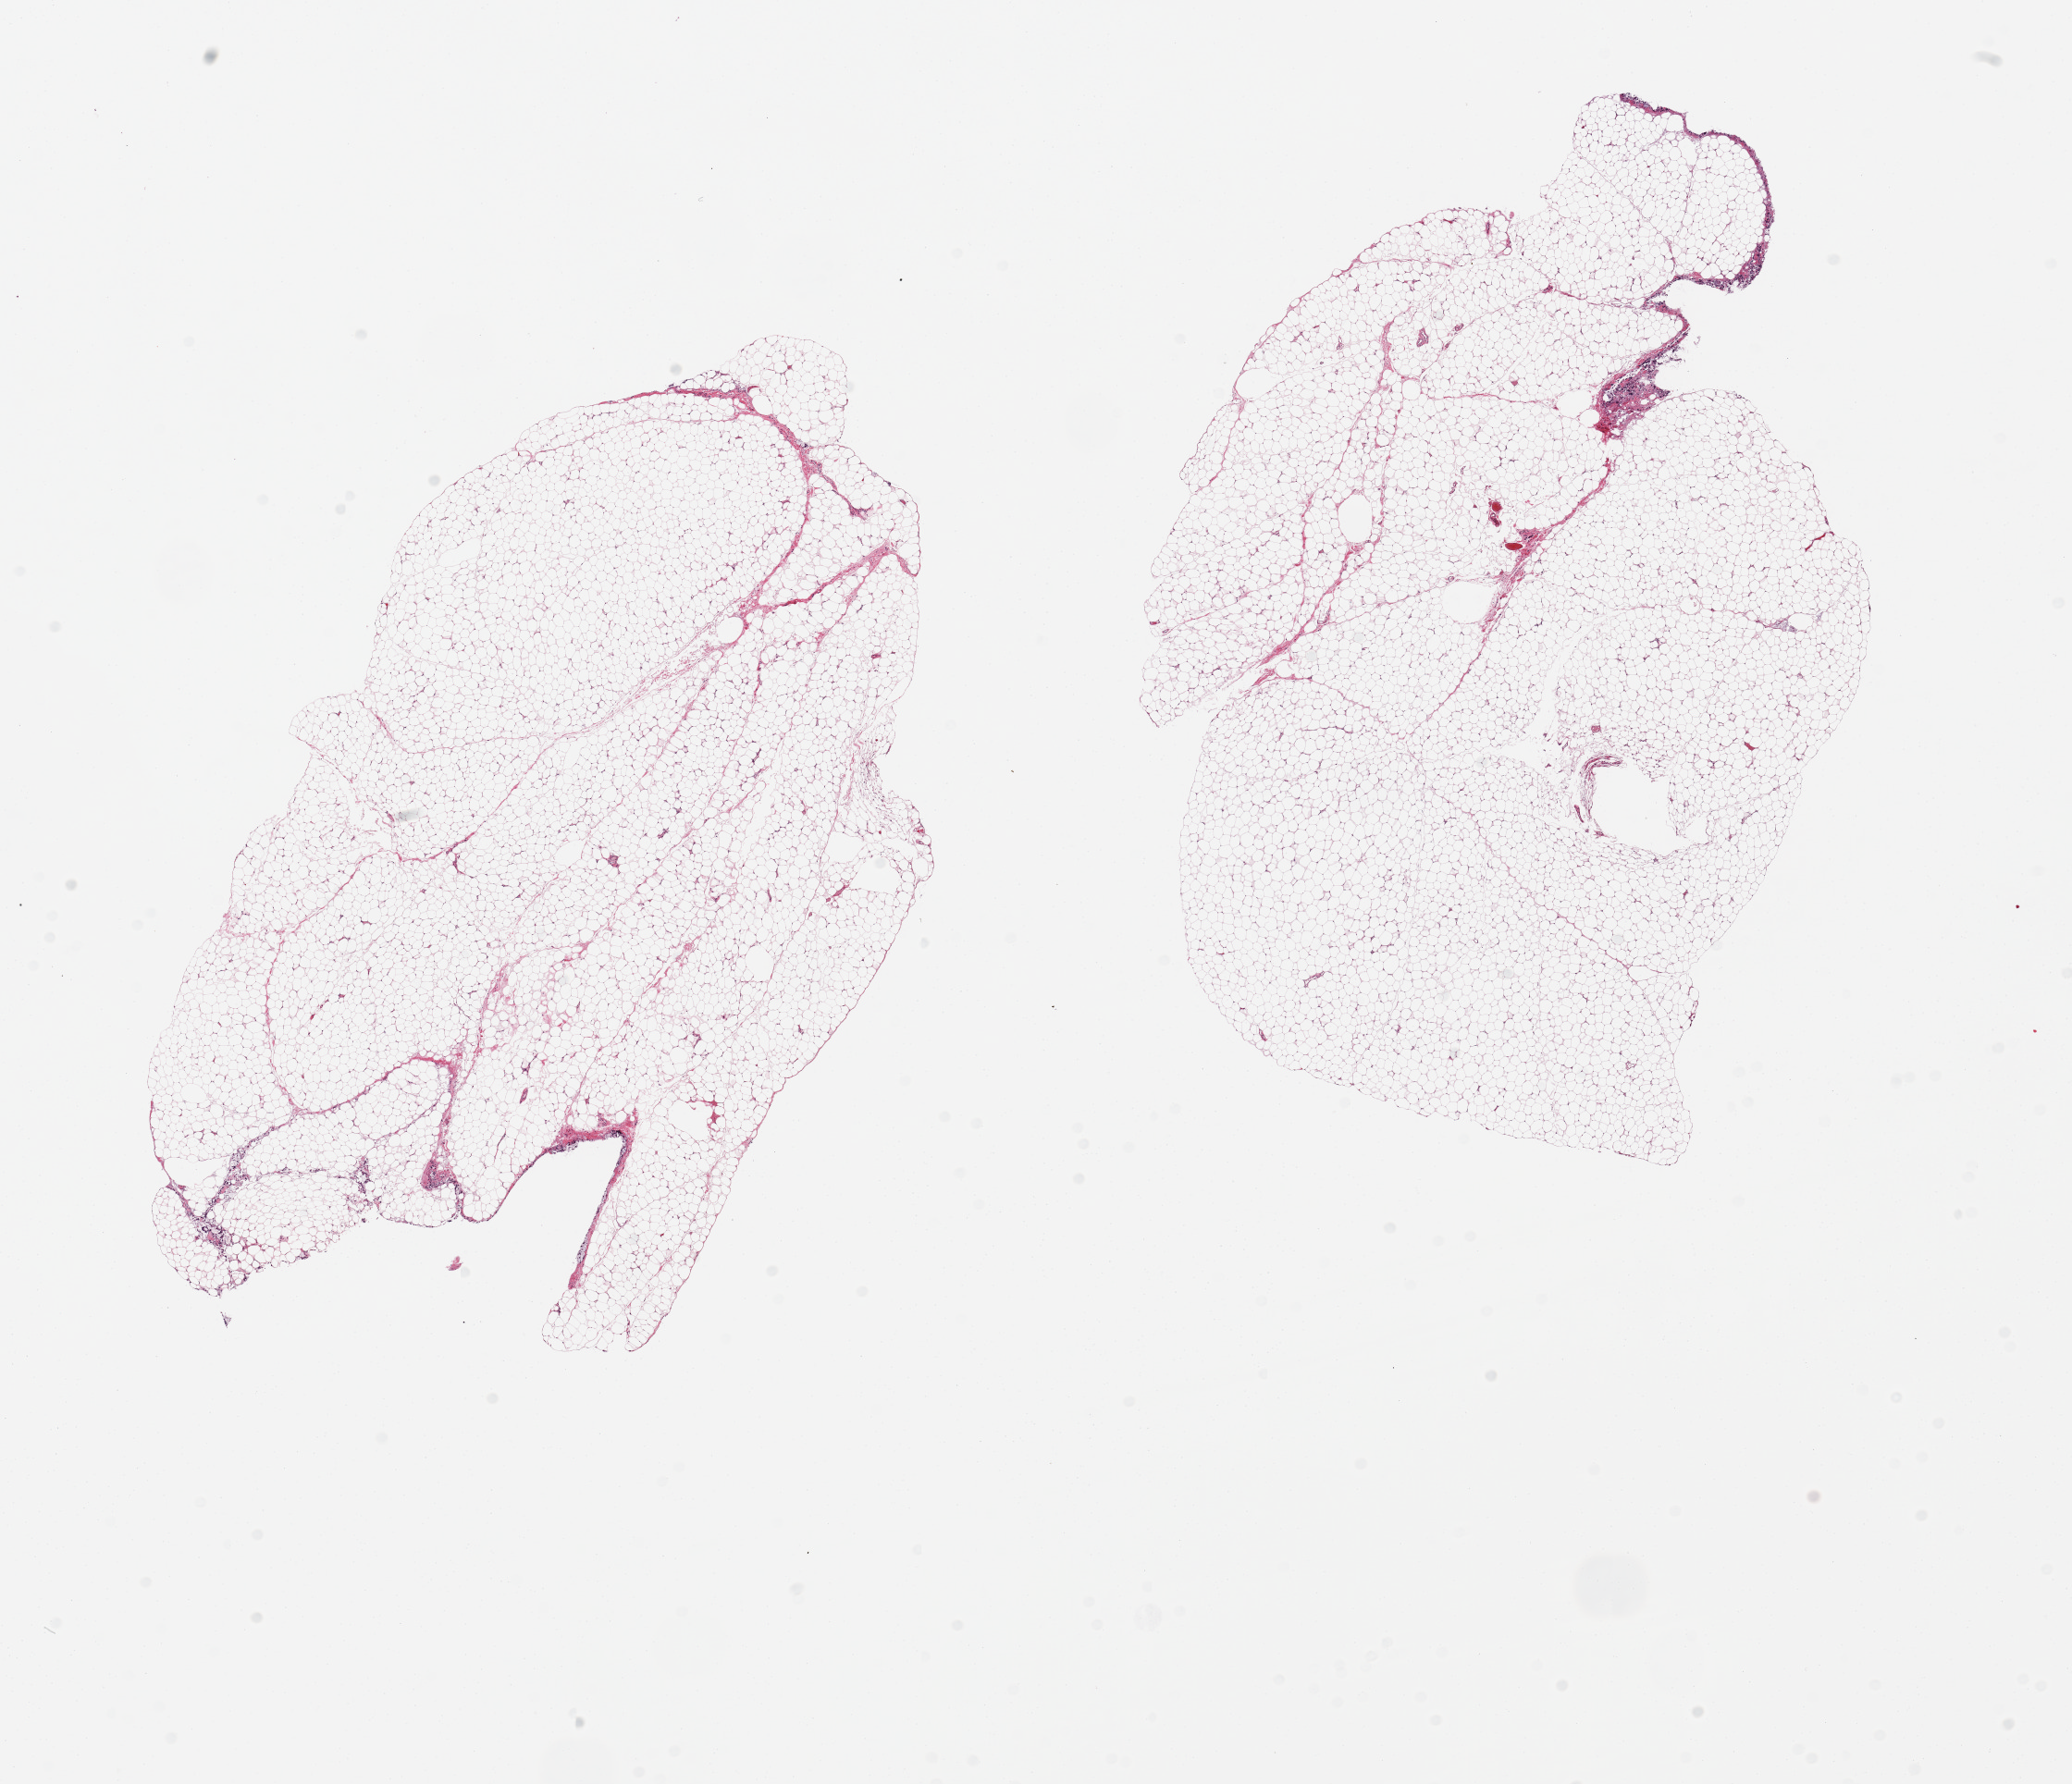
Whole-slide image, haematoxylin and eosin stain, brightfield, shown as a low-resolution overview of the whole scanned area (about 17.7 x 15.3 mm, from a 20x scan), PAXgene-fixed paraffin-embedded (PFPE) section, section of omentum (target tissue), tissue donor sample. Donor sex: male.
- pathologist's review note for this sample: 2 pieces; septal inflammation with histiocytes and fat necrosis